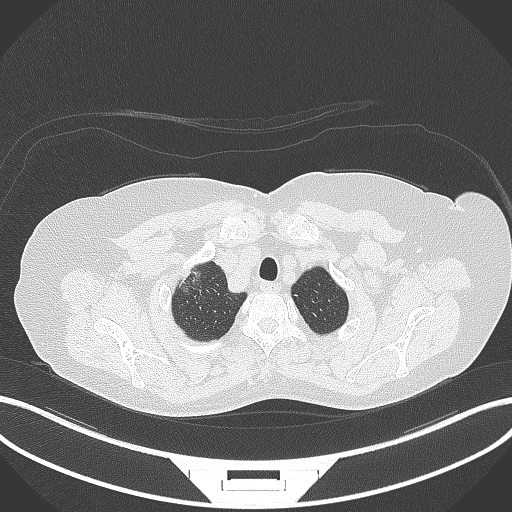
Chest CT, one axial slice. Position 317 of 365 along the scan axis. Lung window (W 1500 / L -600 HU). 1 mm slice thickness. 512 × 512 image matrix. Female patient, age 62 years. Case-level facts recorded for this patient, not image findings: clinical TNM (as recorded): T1c N0 M0.
Outlined on this slice (rectangle marked by the reading radiologist):
- lung tumour (recorded histology: adenocarcinoma): bounding box (x1, y1, x2, y2) in pixels: (179, 264, 205, 297)